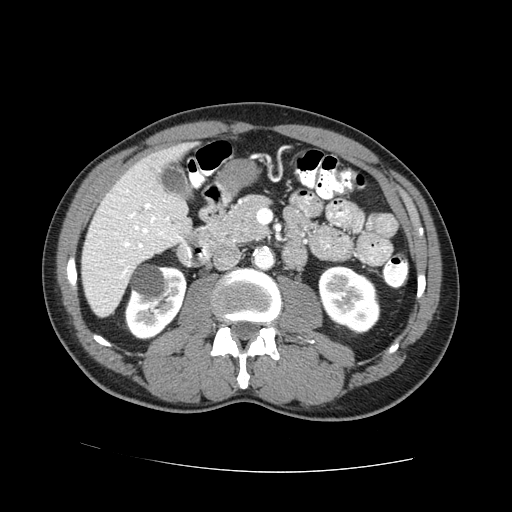
Contrast-enhanced abdominal CT (liver protocol), one axial slice. Position 23 of 73 along the scan axis. Reconstruction kernel STANDARD. One of 2 acquisitions stored at this slice position. Soft-tissue window (W 400 / L 40 HU). 2.5 mm slice thickness. 512 × 512 image matrix, field of view 380 × 380 mm. Case-level facts recorded for this patient, not image findings: diagnosis: hepatocellular carcinoma (patient treated with transarterial chemoembolisation; whether this scan precedes or follows treatment is not stated here); TNM stage (as recorded): Stage-IVA; Child-Pugh class: A; tumour nodularity: uninodular.
Annotated regions visible in this slice (semi-automatically segmented with operator editing):
- liver parenchyma outside the tumour (the mass and vessels are separate outlines, so this box may not span the whole liver): bounding box (x1, y1, x2, y2) in pixels: (82, 142, 194, 316)
- liver vessels: (115, 190, 180, 277)